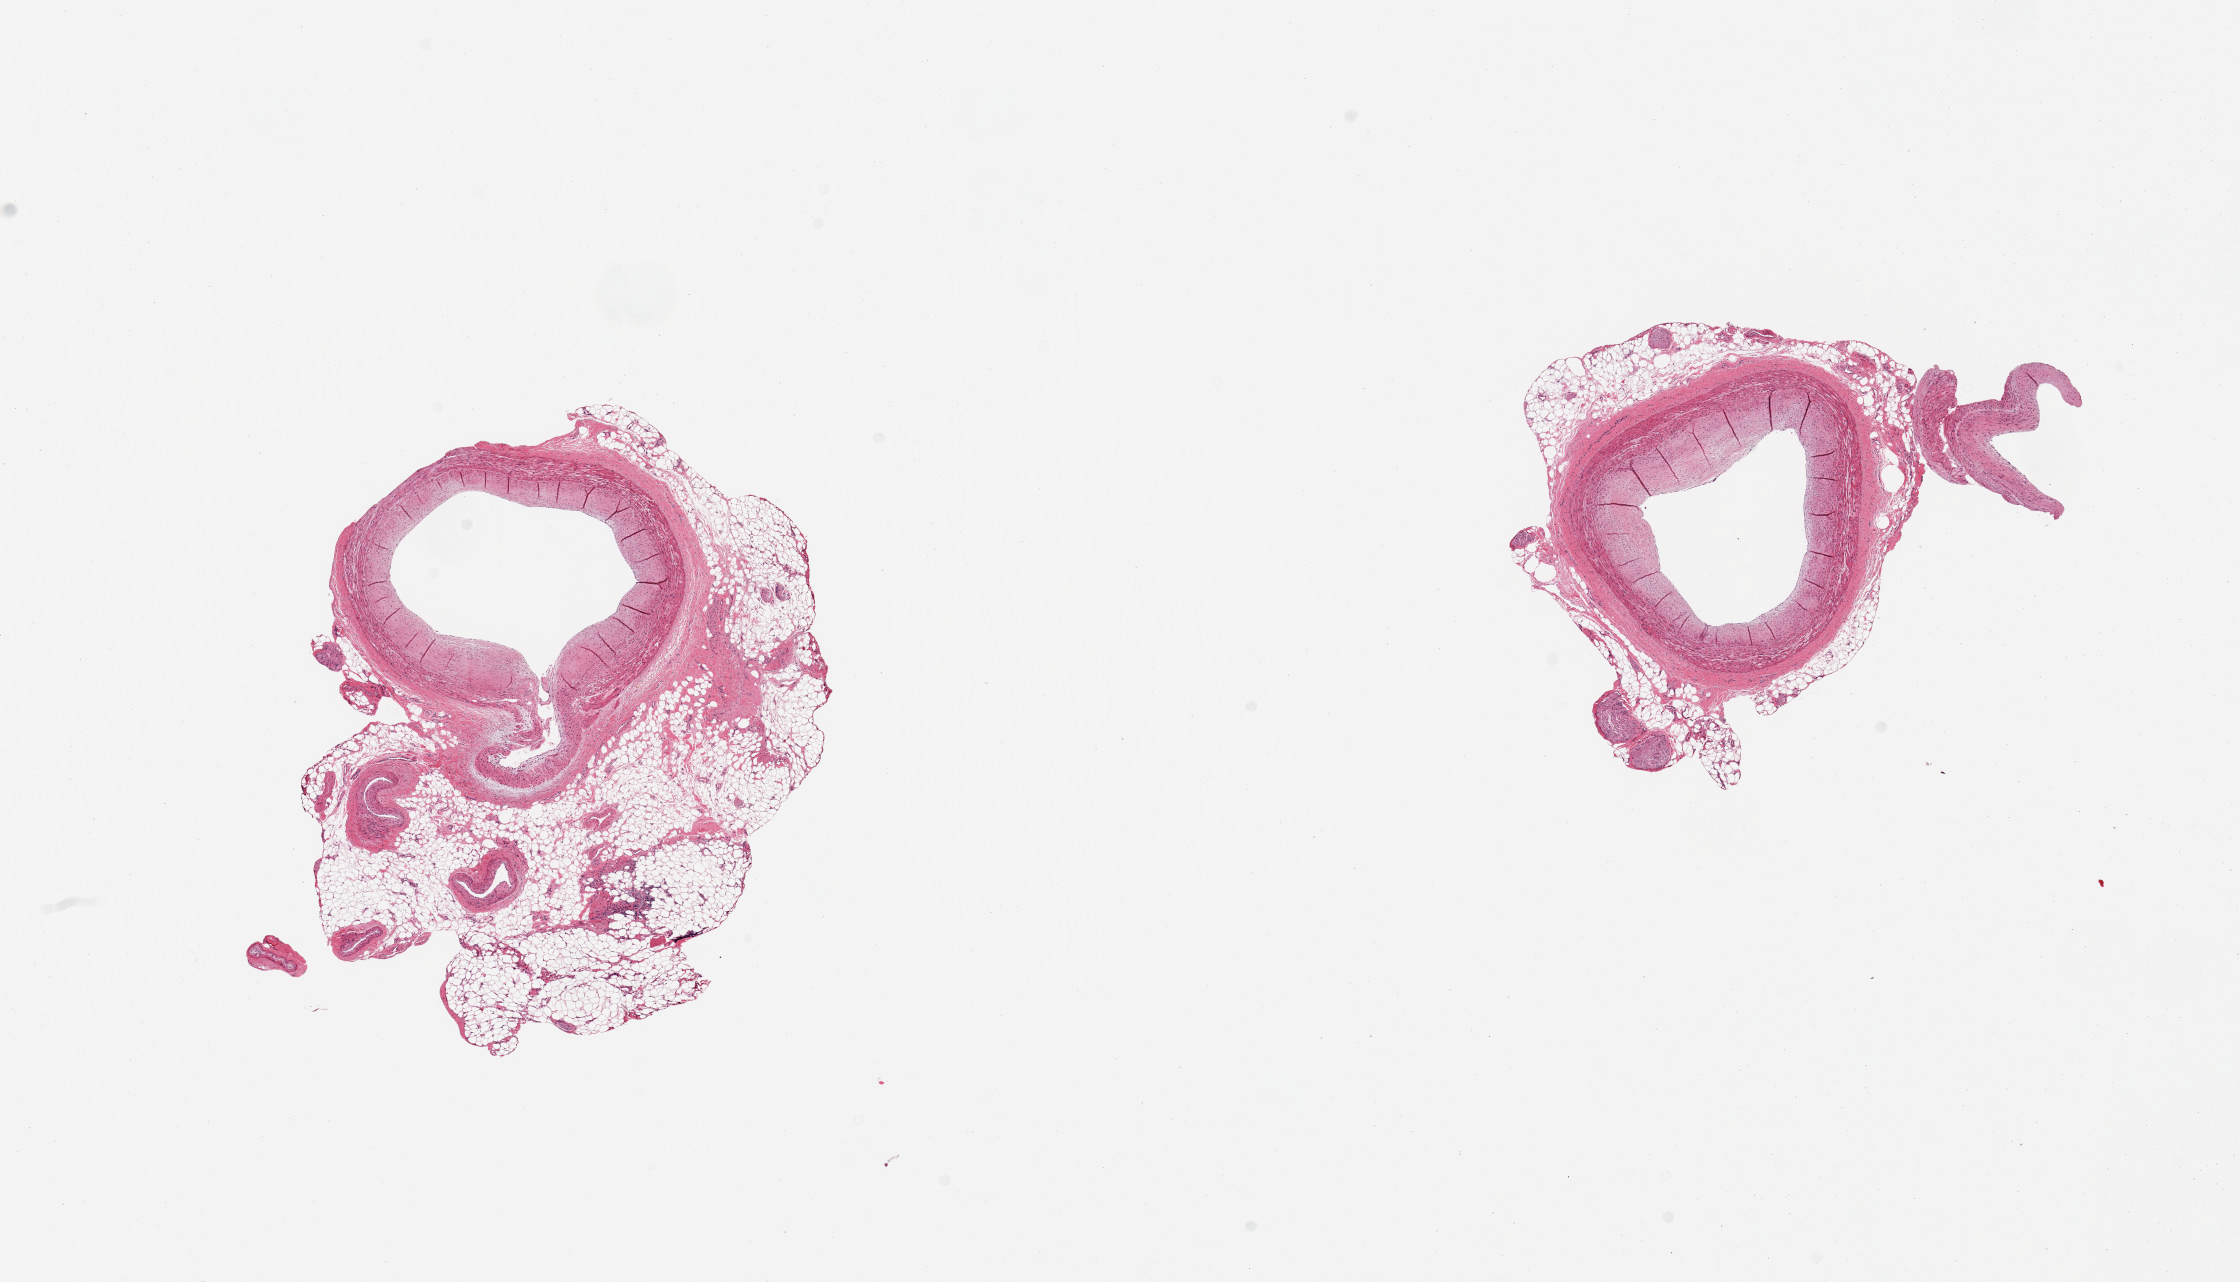
Haematoxylin and eosin whole-slide image — whole scanned area (about 17.7 x 10.1 mm, slide scanned at 20x) shown as a low-resolution overview; PAXgene-fixed paraffin-embedded (PFPE) section; sampled site (target tissue): coronary artery; donor tissue sample.
Review note (as recorded): 2 pieces; mild concentric intimal plaques; 50% & 20% external fat.